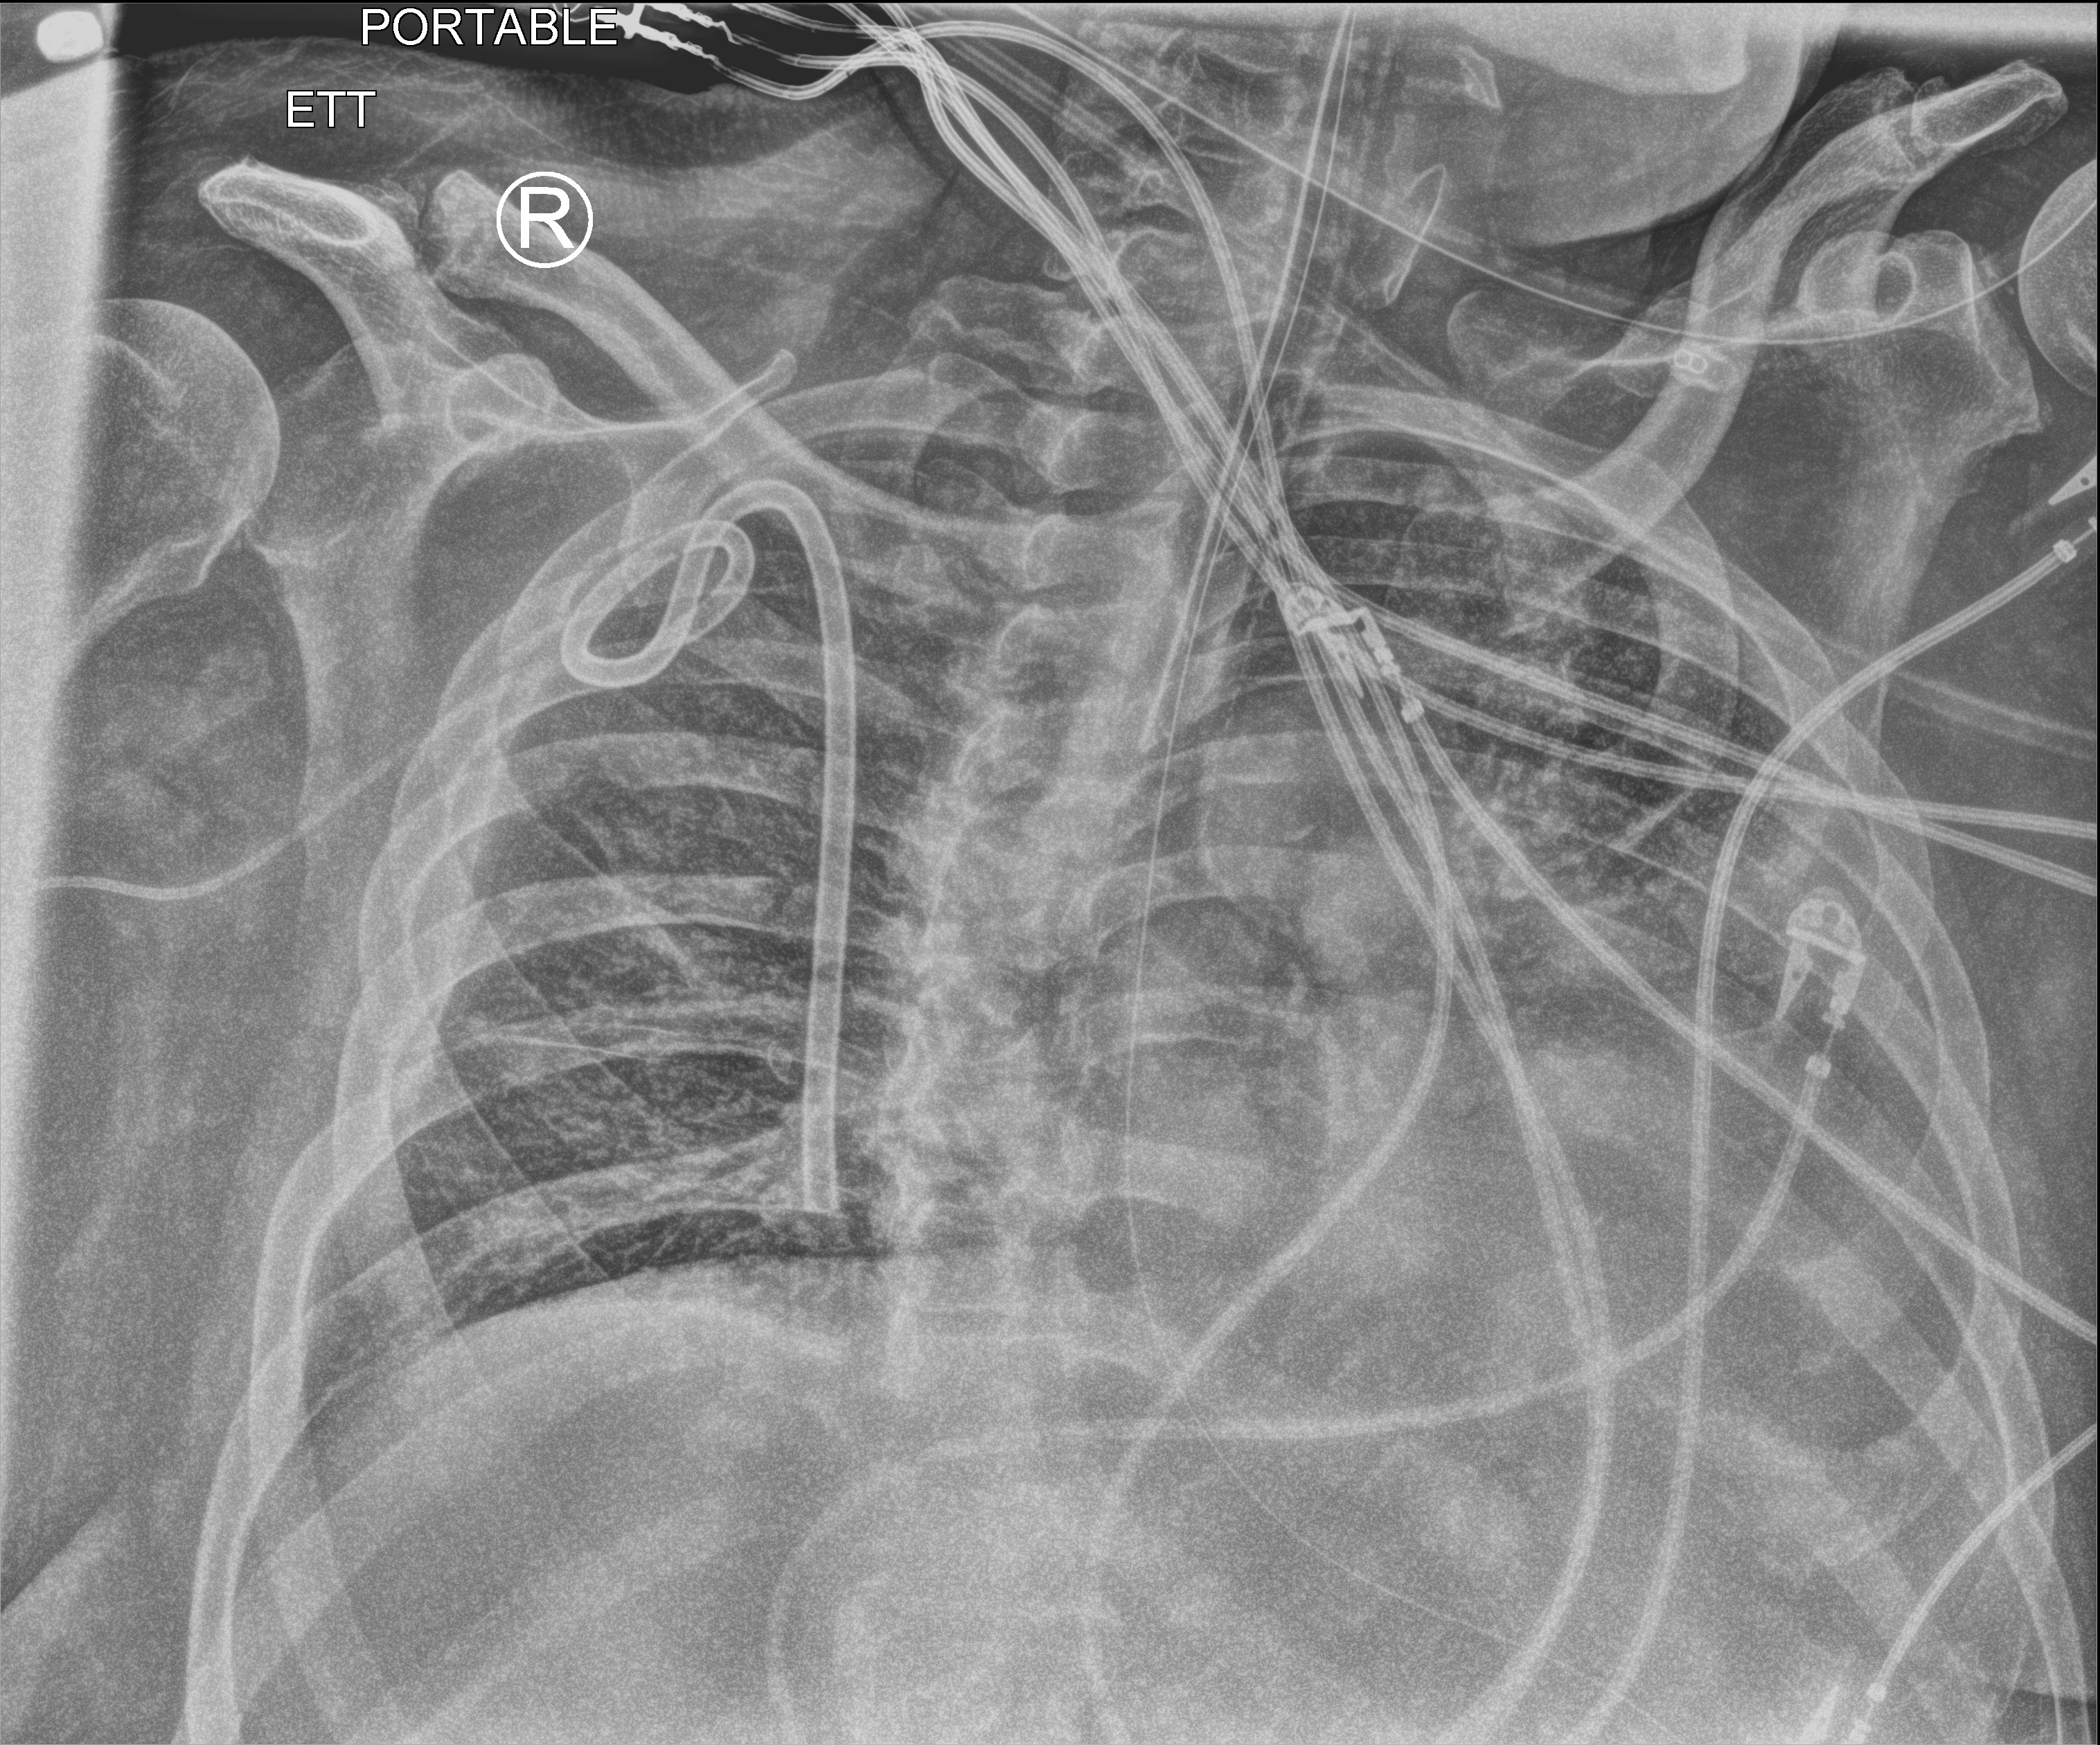
Portable chest radiograph; anteroposterior (AP) projection. Patient hospitalised with COVID-19; male, aged 60–74 years.
Hospital-stay facts (about this admission, not read from this image; timing relative to this image not recorded): mechanically ventilated during this hospital stay: yes.